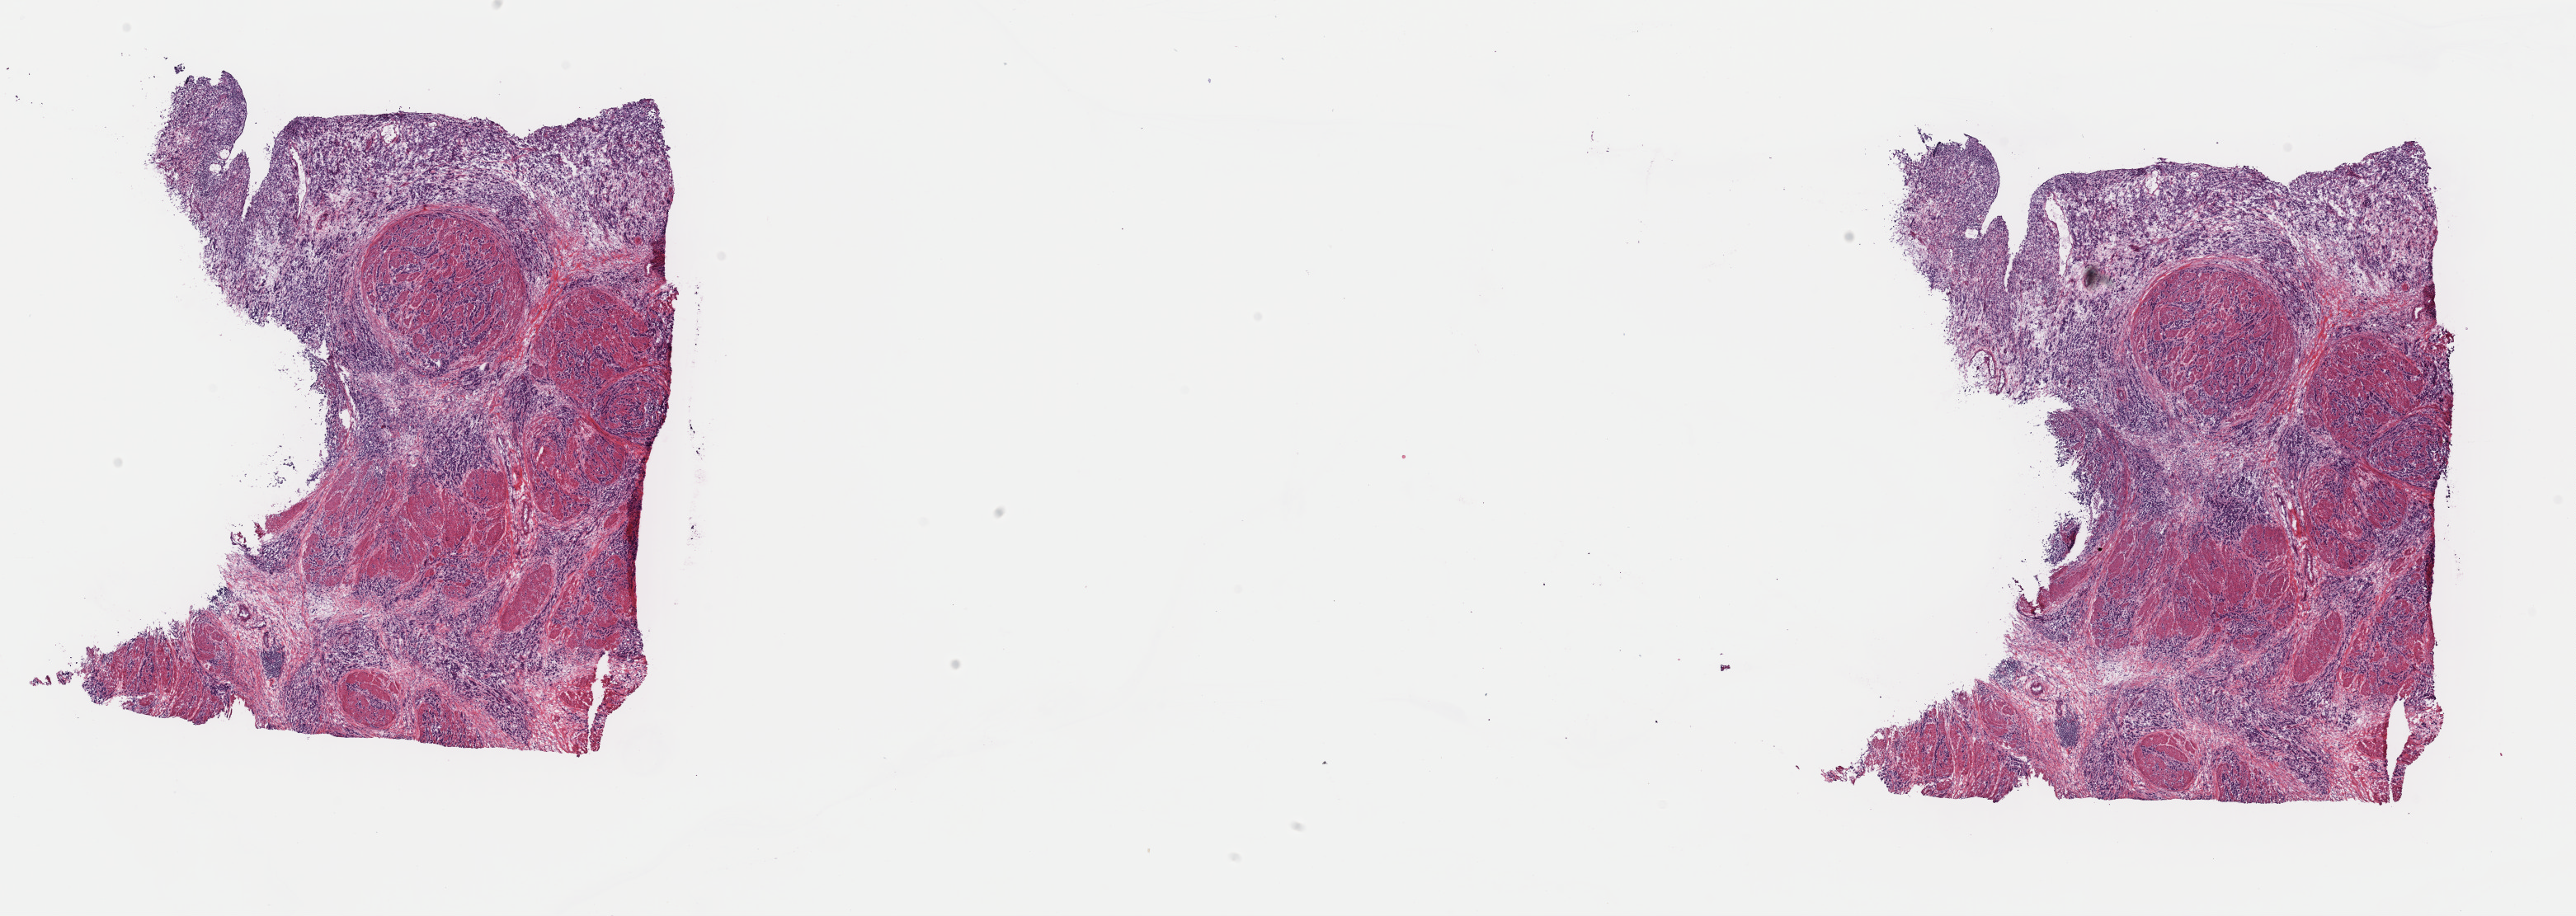
Digitized Hematoxylin and eosin (H&E) stained tissue section (whole slide) — low-resolution overview of the scanned area, about 24.7 x 8.8 mm, frozen section from the top of the tissue portion, bladder, primary tumour sample. Patient: male, age at initial diagnosis 73 years. Histologic grade: high grade. Pathologist review of this section (percent, as recorded): tumour cells 60%, tumour nuclei 75%, normal cells 0%, stromal cells 40%, necrosis 0%. Inflammatory infiltration, as recorded: lymphocyte infiltration 0%, monocyte infiltration 0%, neutrophil infiltration 0%.
Diagnosis: Transitional cell carcinoma (lateral wall of bladder). AJCC pathologic stage: IV.